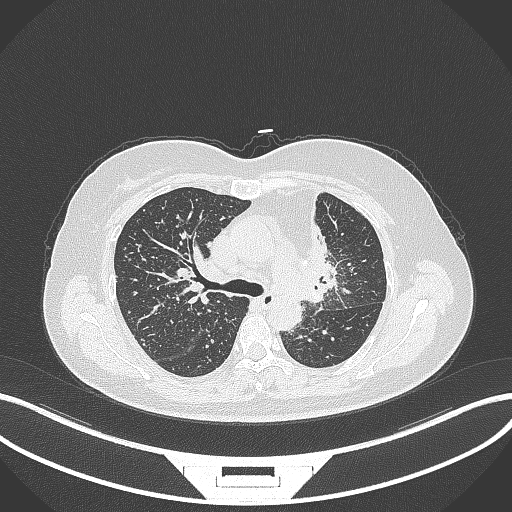
Chest CT, one axial slice. Slice 219 of 348 in the series (ordered by position). 120 kVp. Lung window (W 1500 / L -600 HU). 1 mm slice thickness. 512 × 512 image matrix. Female patient, age 49 years. From the clinical record (not read from this slice): clinical TNM (as recorded): T1c N0 M1.
Structures marked on this image (bounding box drawn by a radiologist):
- lung tumour (recorded histology: adenocarcinoma): bounding box <296,195,339,310> (left, top, right, bottom; pixels)